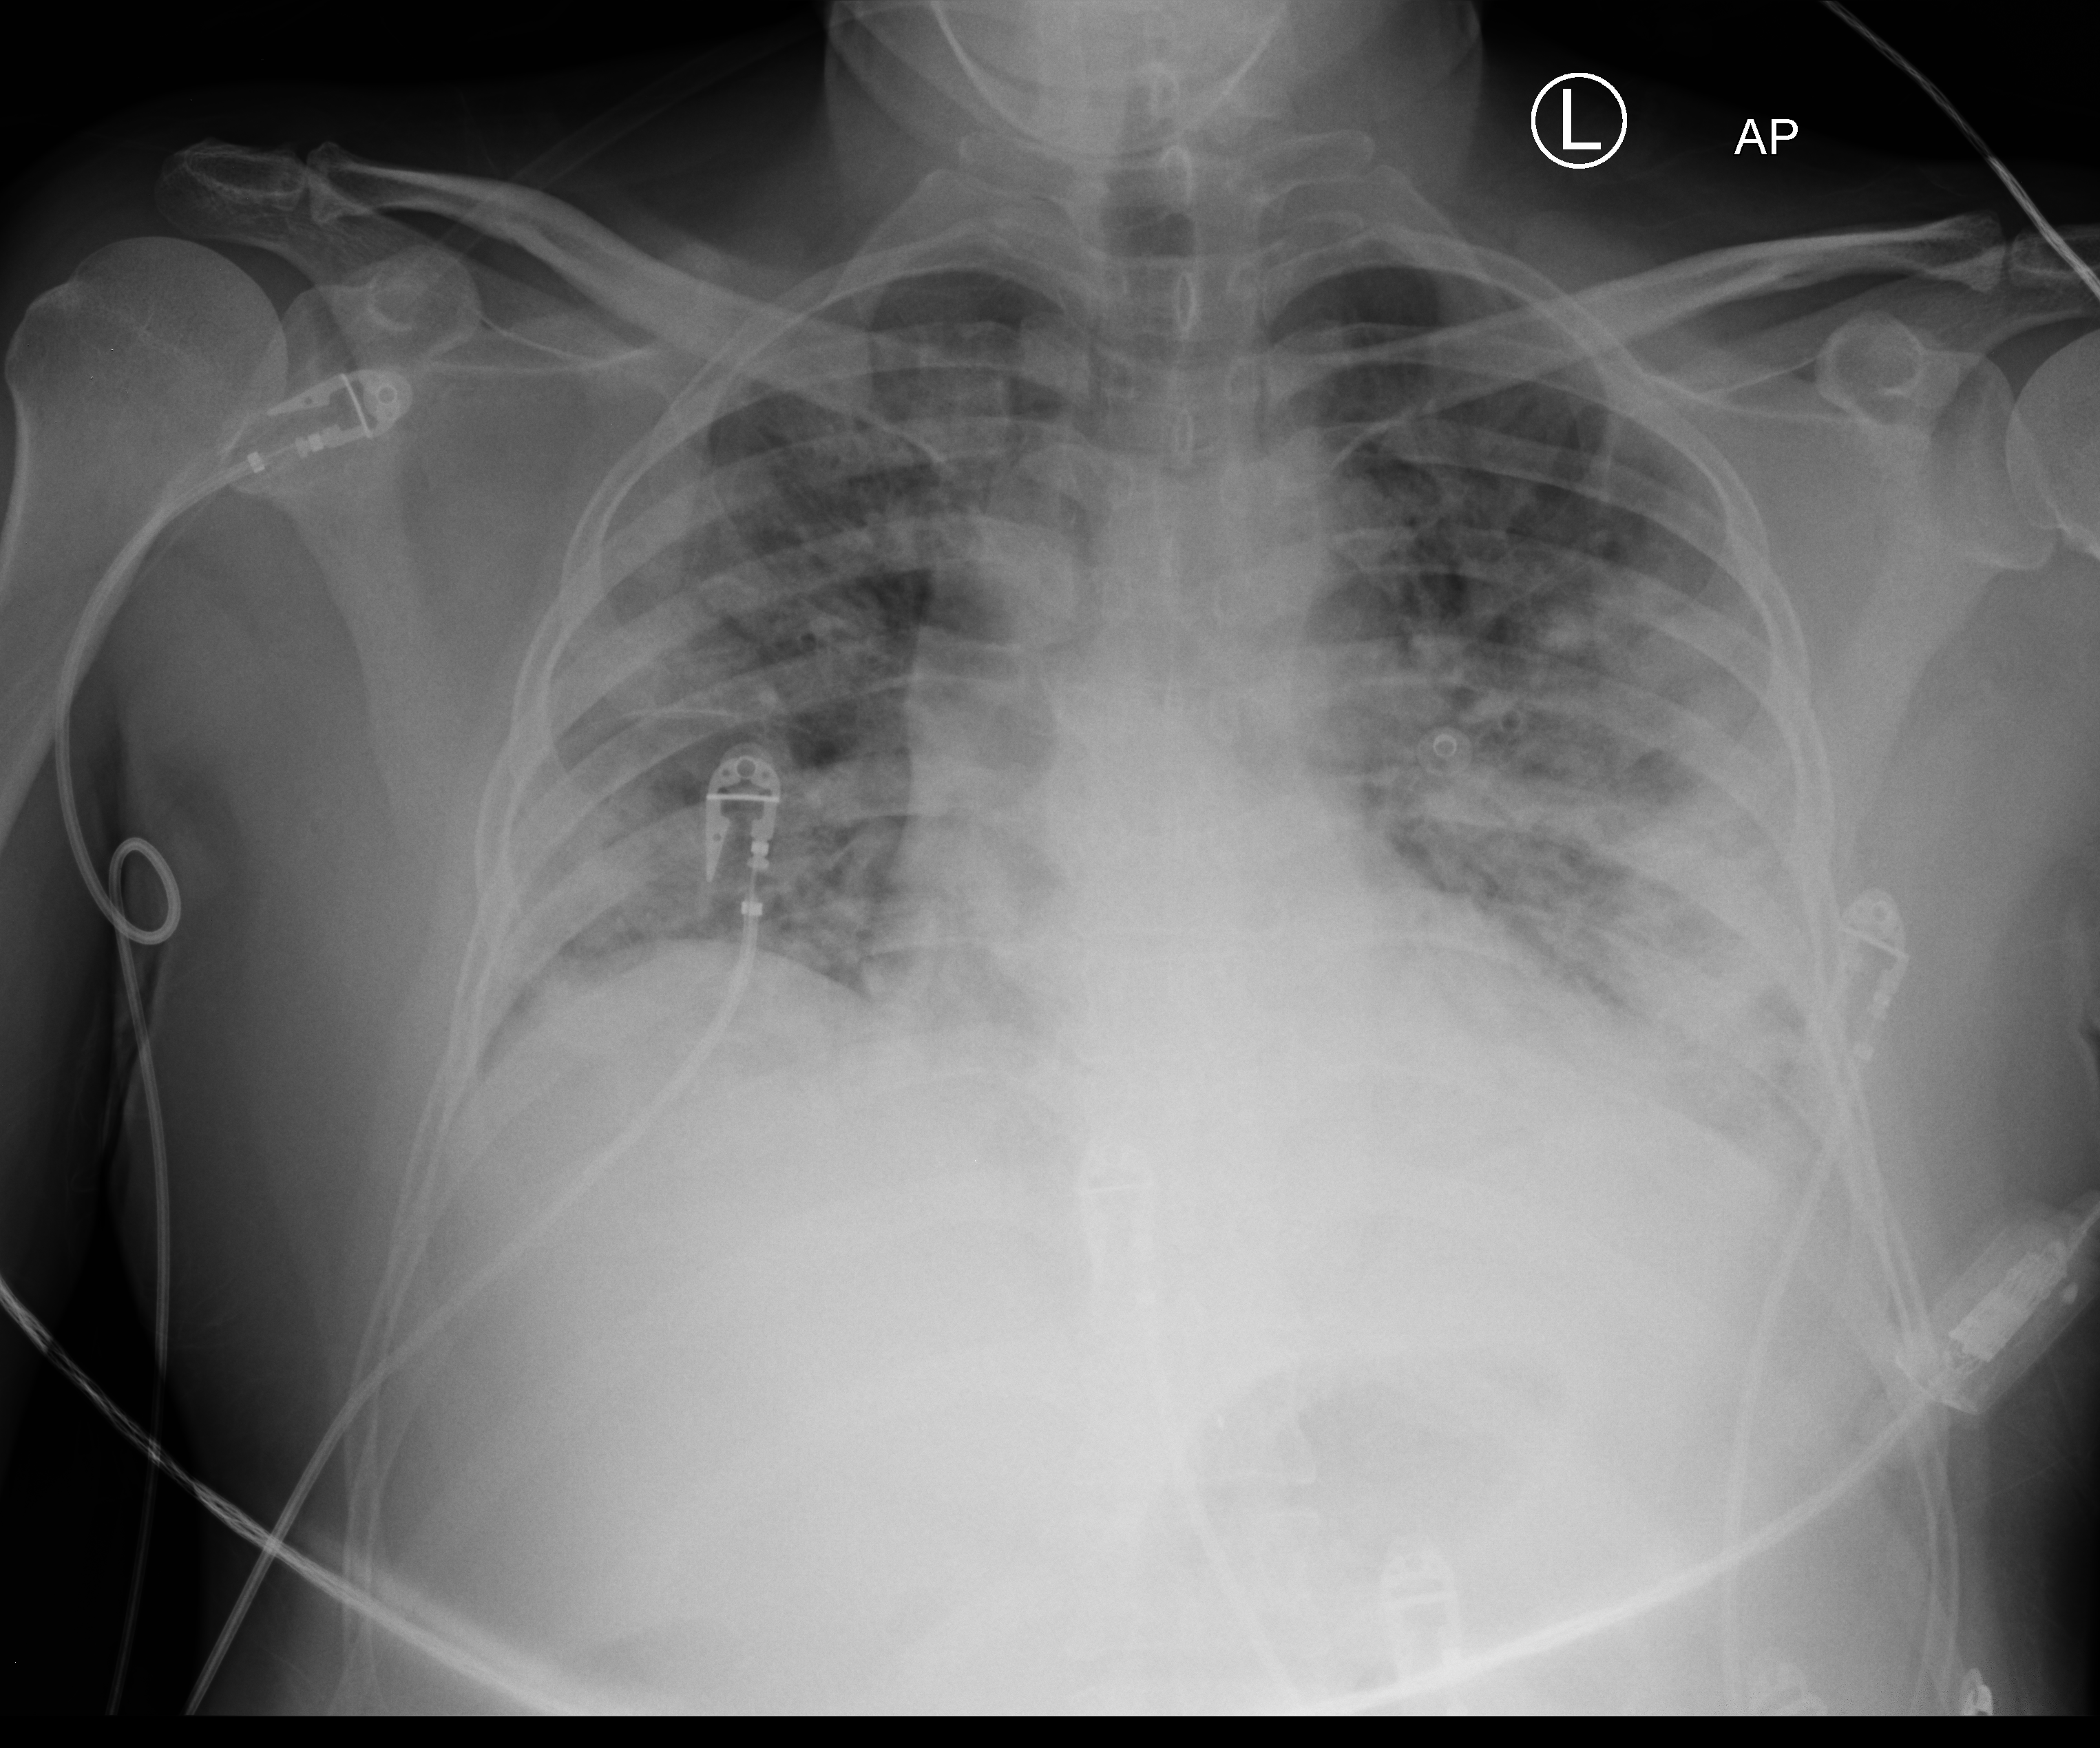
Bedside chest radiograph (computed radiography), anteroposterior (AP) projection. Patient hospitalised with COVID-19; male, aged 18–59 years.
Admission-level facts for this patient (not findings on this image; timing relative to this image not recorded): admitted to intensive care during this hospital stay: yes; COPD (admission record): no; length of hospital stay: 16 days.